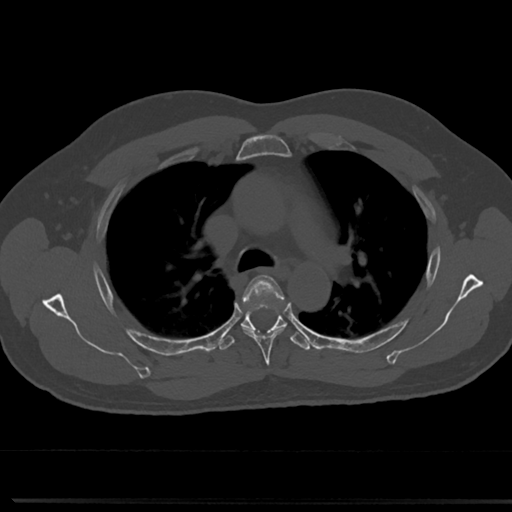
CT including the spine, one axial slice; position 525 of 817 along the scan axis; reconstruction kernel Br40s/3; 120 kVp; bone window (W 1800 / L 400 HU); 512 × 512 image matrix, field of view 355 × 355 mm. Male patient, age 61 years. From the clinical record (not read from this slice): primary cancer: prostate.
Outlined on this slice (semi-automatically segmented with operator editing):
- T4 vertebra: bounding box (x1, y1, x2, y2) in pixels: (238, 275, 289, 358)
- T5 vertebra: (241, 320, 307, 345)